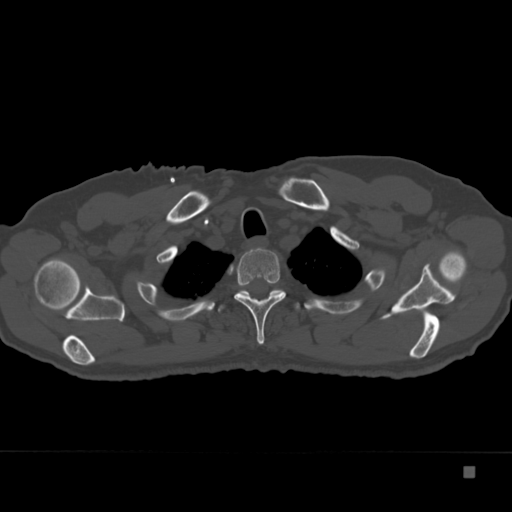
CT including the spine, one axial slice; position 299 of 332 along the scan axis; 120 kVp; bone window (W 1800 / L 400 HU); 512 × 512 image matrix, field of view 389 × 389 mm. Male patient, age 72 years. From the clinical record (not read from this slice): primary cancer: skeletal.
Annotated regions visible in this slice (semi-automatic segmentation, software-assisted and operator-edited):
- T2 vertebra: box from (x=234, y=248) to (x=285, y=345) px
- T3 vertebra: (x=218, y=285)–(x=299, y=312)